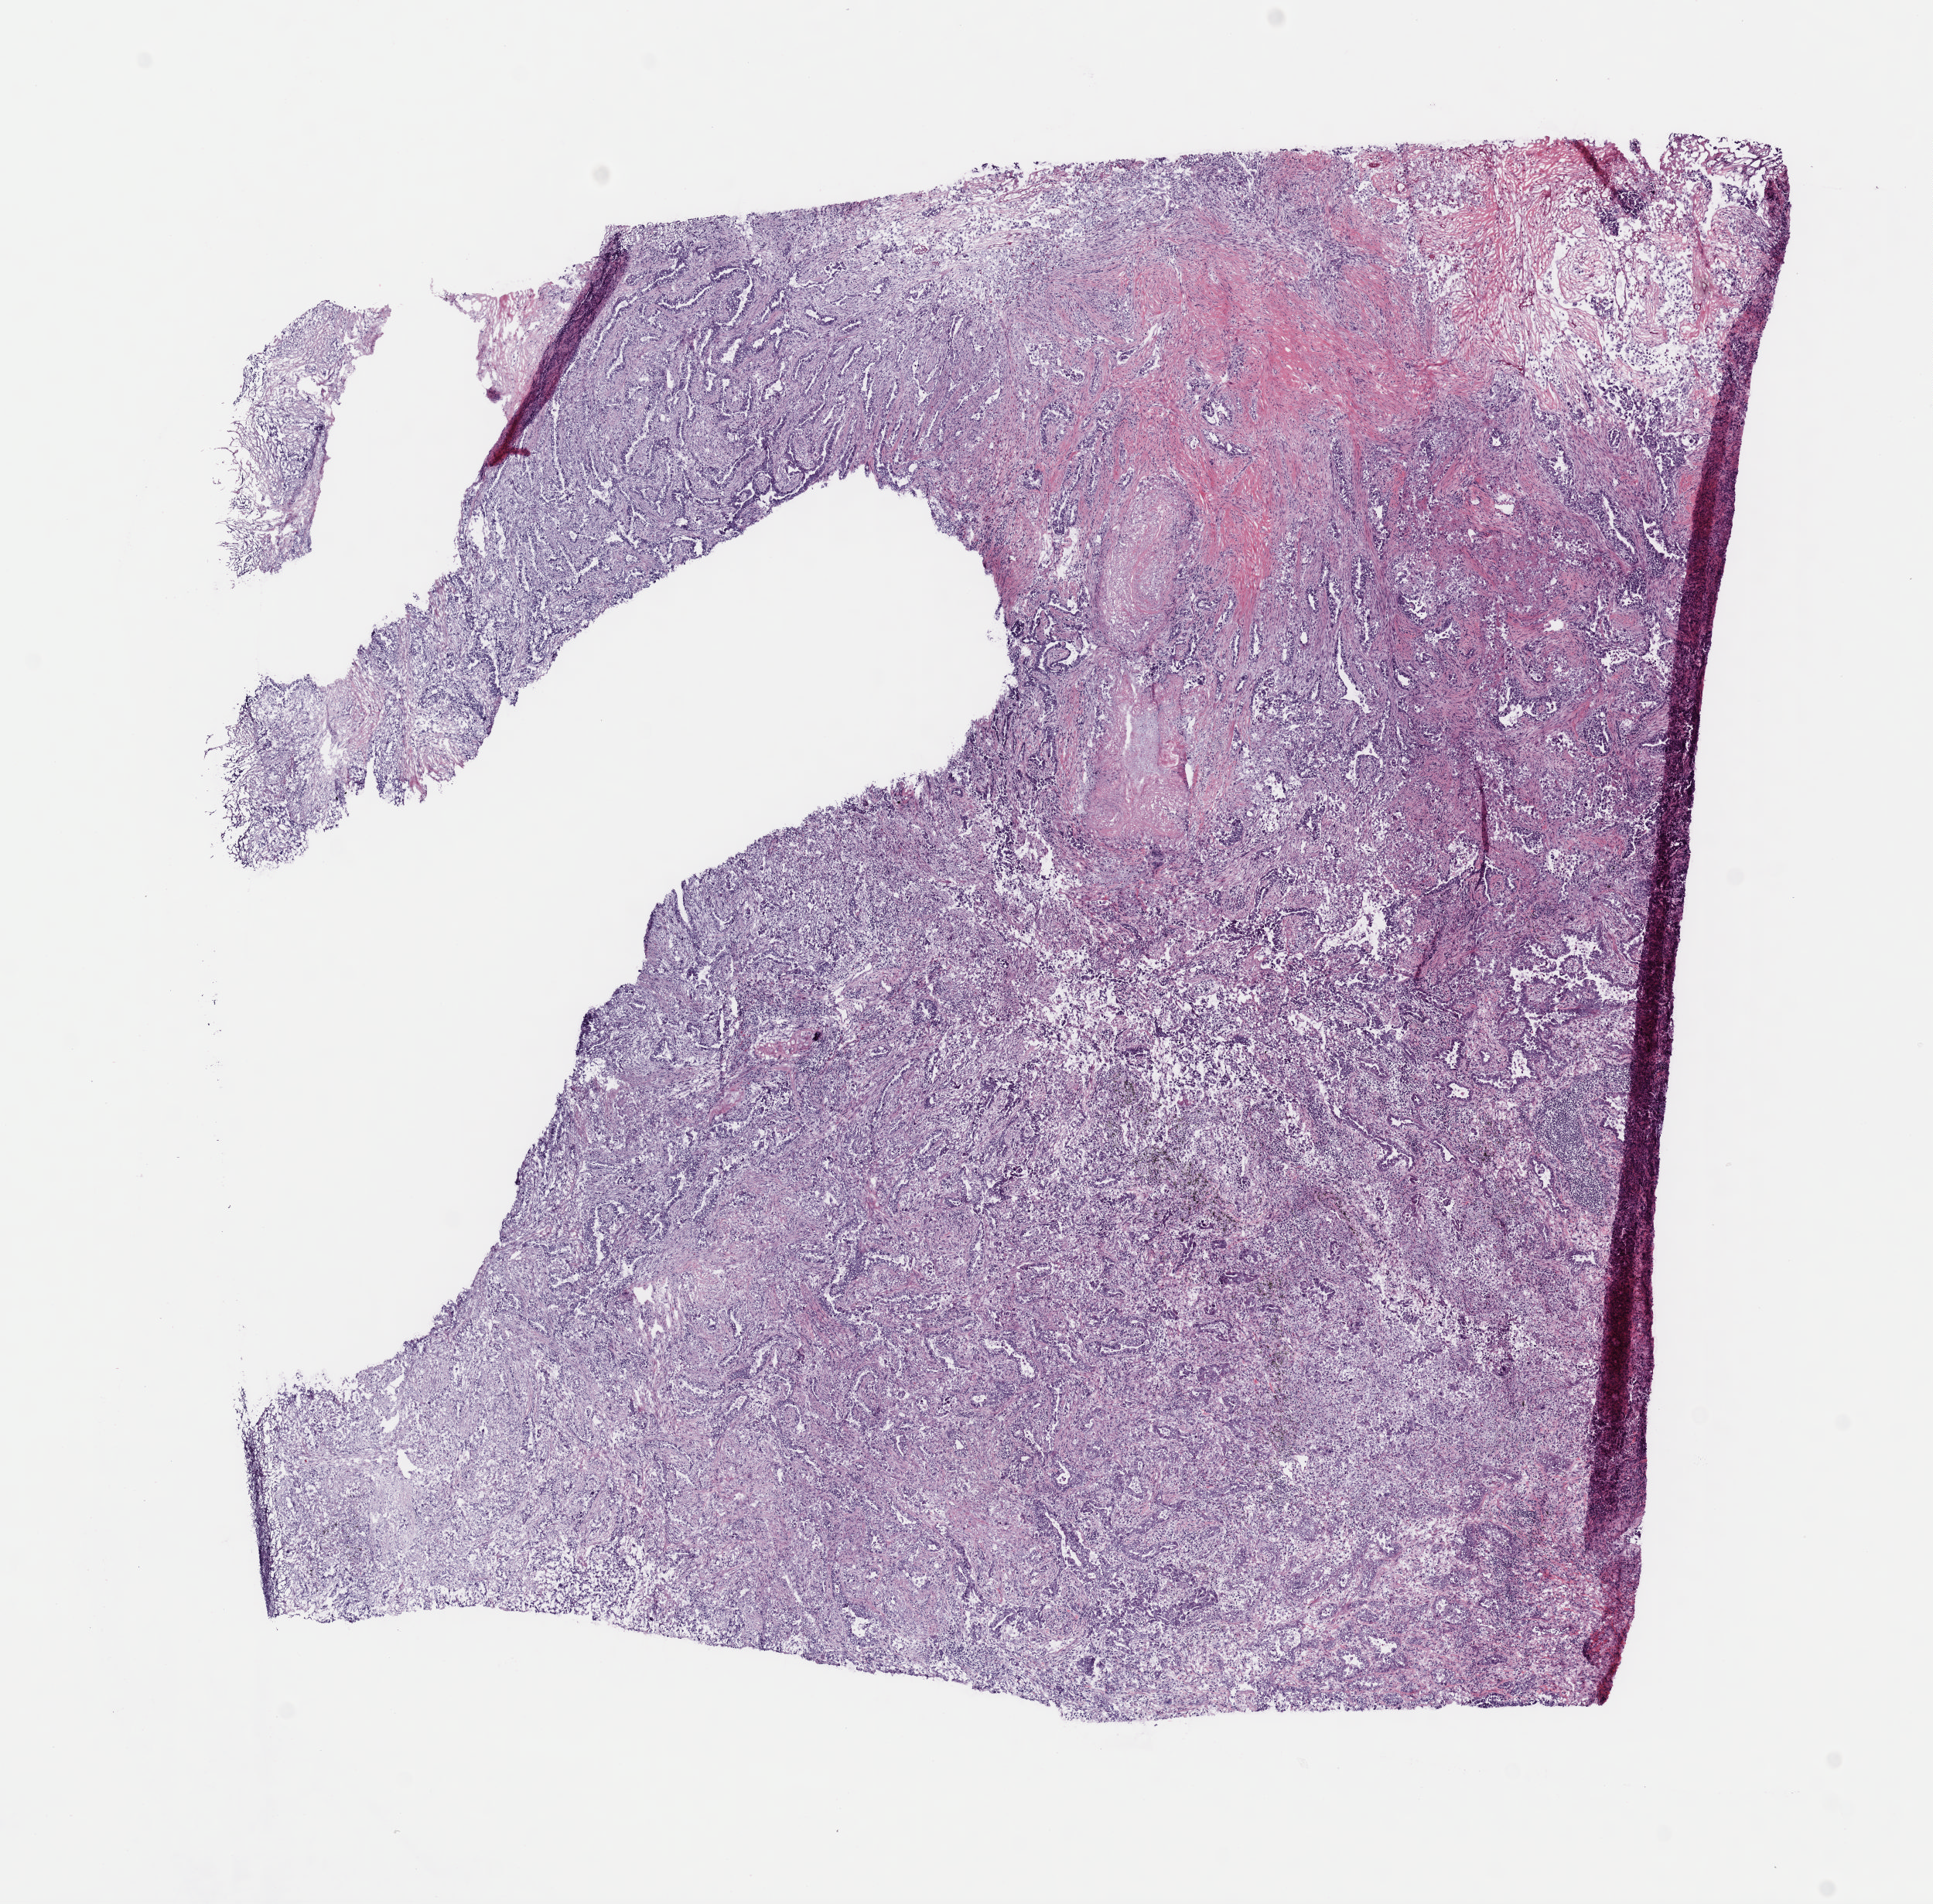
Digitized Hematoxylin and eosin (H&E) stained tissue section (whole slide), shown as a low-resolution overview of the whole scanned area (about 9.9 x 9.7 mm, from a 40x scan). Frozen section from the top of the tissue portion. Sample: primary tumour, lung. Patient: female, age at initial diagnosis 72 years. Composition of this section per pathologist review: tumour cells 80%, tumour nuclei 80%, normal cells 0%, stromal cells 10%, necrosis 10%. Infiltration values recorded for this section: lymphocyte infiltration 40%, monocyte infiltration 20%, neutrophil infiltration 20%.
- AJCC pathologic stage: IB (7th edition)
- diagnosis: Adenocarcinoma, NOS (upper lobe, lung)